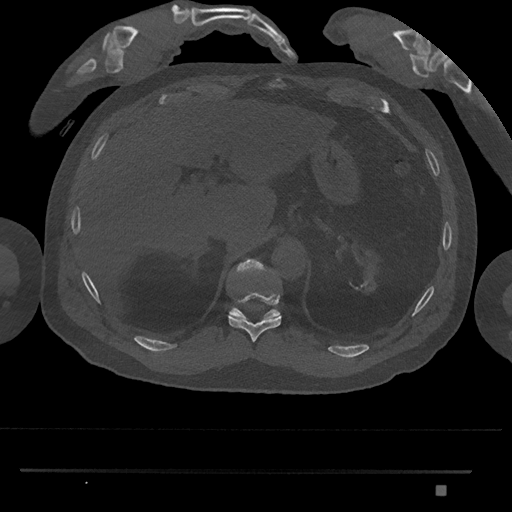
CT including the spine, one axial slice; slice 985 of 1134 in the series (ordered by position); reconstruction kernel Br40s/3; bone window (W 1800 / L 400 HU); 0.5 mm slice thickness; 512 × 512 image matrix, field of view 429 × 429 mm. Male patient, age 65 years. From the clinical record (not read from this slice): primary cancer: prostate.
Outlined on this slice (semi-automatic segmentation, software-assisted and operator-edited):
- T10 vertebra: box from (x=228, y=293) to (x=281, y=343) px
- T11 vertebra: (x=229, y=259)–(x=281, y=319)